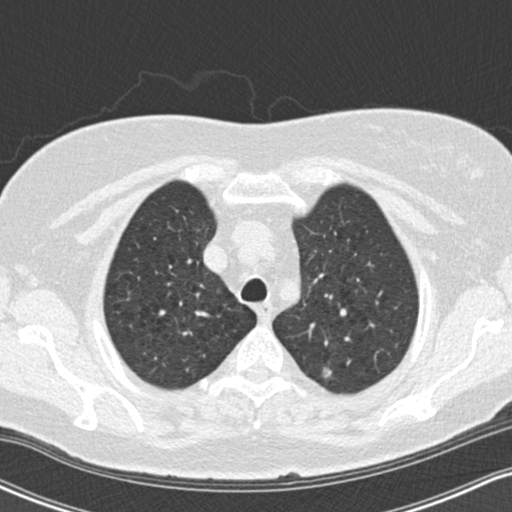
Low-dose screening chest CT, one axial slice; 120 kVp; lung window (W 1500 / L -600 HU); 2 mm slice thickness; 512 × 512 image matrix, field of view 320 × 320 mm.
Annotated regions visible in this slice (outlined manually by an expert reader):
- lesion 1 (tumor, upper lobe of left lung): bounding box [x1, y1, x2, y2] px = [323, 366, 332, 378]